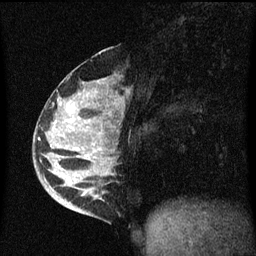
Breast MRI (dynamic contrast-enhanced), one sagittal slice. Slice 23 of 60 in the series (ordered by position). Dynamic contrast-enhanced series, image 2 of 3 at this slice position (ordered by acquisition). 1.5 T. TE 4.2 ms, TR 8.4 ms. 2 mm slice thickness. 256 × 256 image matrix, field of view 200 × 200 mm. Patient: female, 34 years. Case-level facts recorded for this patient, not image findings: setting: breast cancer imaged before/during neoadjuvant chemotherapy; receptor status: HR-positive, HER2-negative.
Outlined on this slice (semi-automatically segmented with operator editing):
- analysis volume of interest (the breast-tissue region the enhancement analysis was run in; not a lesion): bounding box <34,48,119,215> (left, top, right, bottom; pixels)
- tumour enhancement mask (voxels above the 70 % enhancement threshold inside the analysis volume of interest): <70,120,75,123>